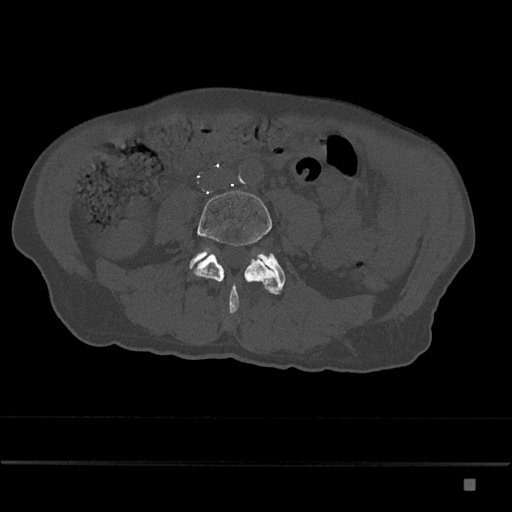
CT including the spine, one axial slice. Slice 324 of 797 in the series (ordered by position). 120 kVp. Bone window (W 1800 / L 400 HU). 0.5 mm slice thickness. 512 × 512 image matrix, field of view 390 × 390 mm. Patient: male, 72 years. Case-level facts recorded for this patient, not image findings: primary cancer: prostate.
Outlined on this slice (semi-automatic segmentation, software-assisted and operator-edited):
- L4 vertebra: bounding box [x1, y1, x2, y2] px = [190, 191, 277, 314]
- L5 vertebra: [190, 247, 286, 294]